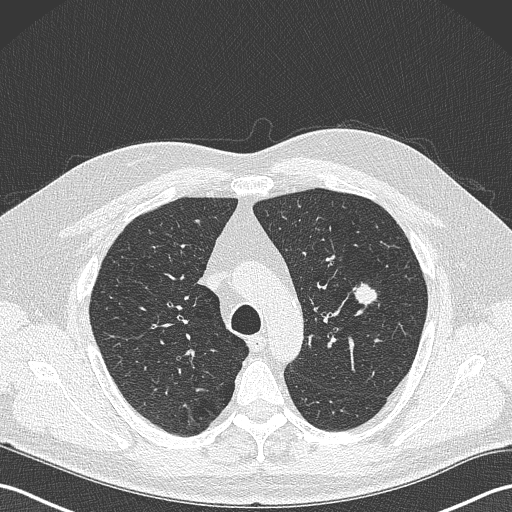
Chest CT (low-dose screening protocol), one axial image. Baseline annual screen. Lung window (W 1500 / L -600 HU). 1 mm slice thickness. Lung (sharp) reconstruction kernel (B50f). Slice 94 of 343 in the series. Male participant, aged 61 years at enrolment. Former smoker at enrolment.
Expert reader's lesion annotation, bounding box (x1, y1, x2, y2) in pixels: (346, 279, 385, 314). The screening reader recorded 2 non-calcified nodules or masses ≥4 mm on this exam (left upper lobe, lingula); which of them this box marks is not recorded. Later outcome: lung cancer diagnosed 160 days after this screen — adenocarcinoma, NOS, left upper lobe, poorly differentiated (G3), stage IA (AJCC 6th edition), 28 mm at pathology.